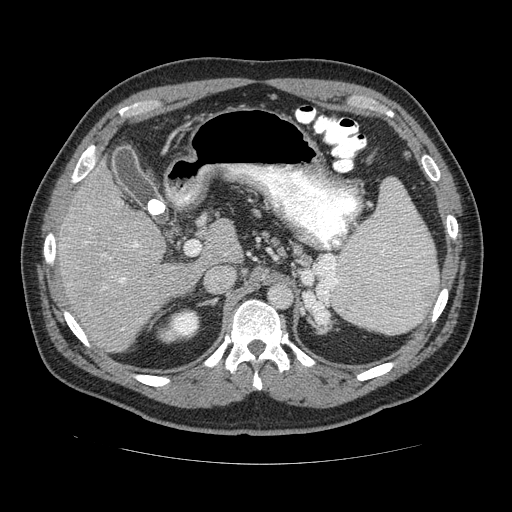
Contrast-enhanced abdominal CT (liver protocol), one axial slice; slice 79 of 113 in the series (ordered by position); 120 kVp; soft-tissue window (W 400 / L 40 HU); 512 × 512 image matrix, field of view 400 × 400 mm. From the clinical record (not read from this slice): diagnosis: hepatocellular carcinoma (patient treated with transarterial chemoembolisation; whether this scan precedes or follows treatment is not stated here); TNM stage (as recorded): Stage-II; Child-Pugh class: B; tumour nodularity: multinodular; tumour size: 4.8 cm.
Structures marked on this image (semi-automatic segmentation, software-assisted and operator-edited):
- liver parenchyma outside the tumour (the mass and vessels are separate outlines, so this box may not span the whole liver): box from (x=52, y=162) to (x=214, y=352) px
- liver vessels: (x=51, y=228)–(x=140, y=289)